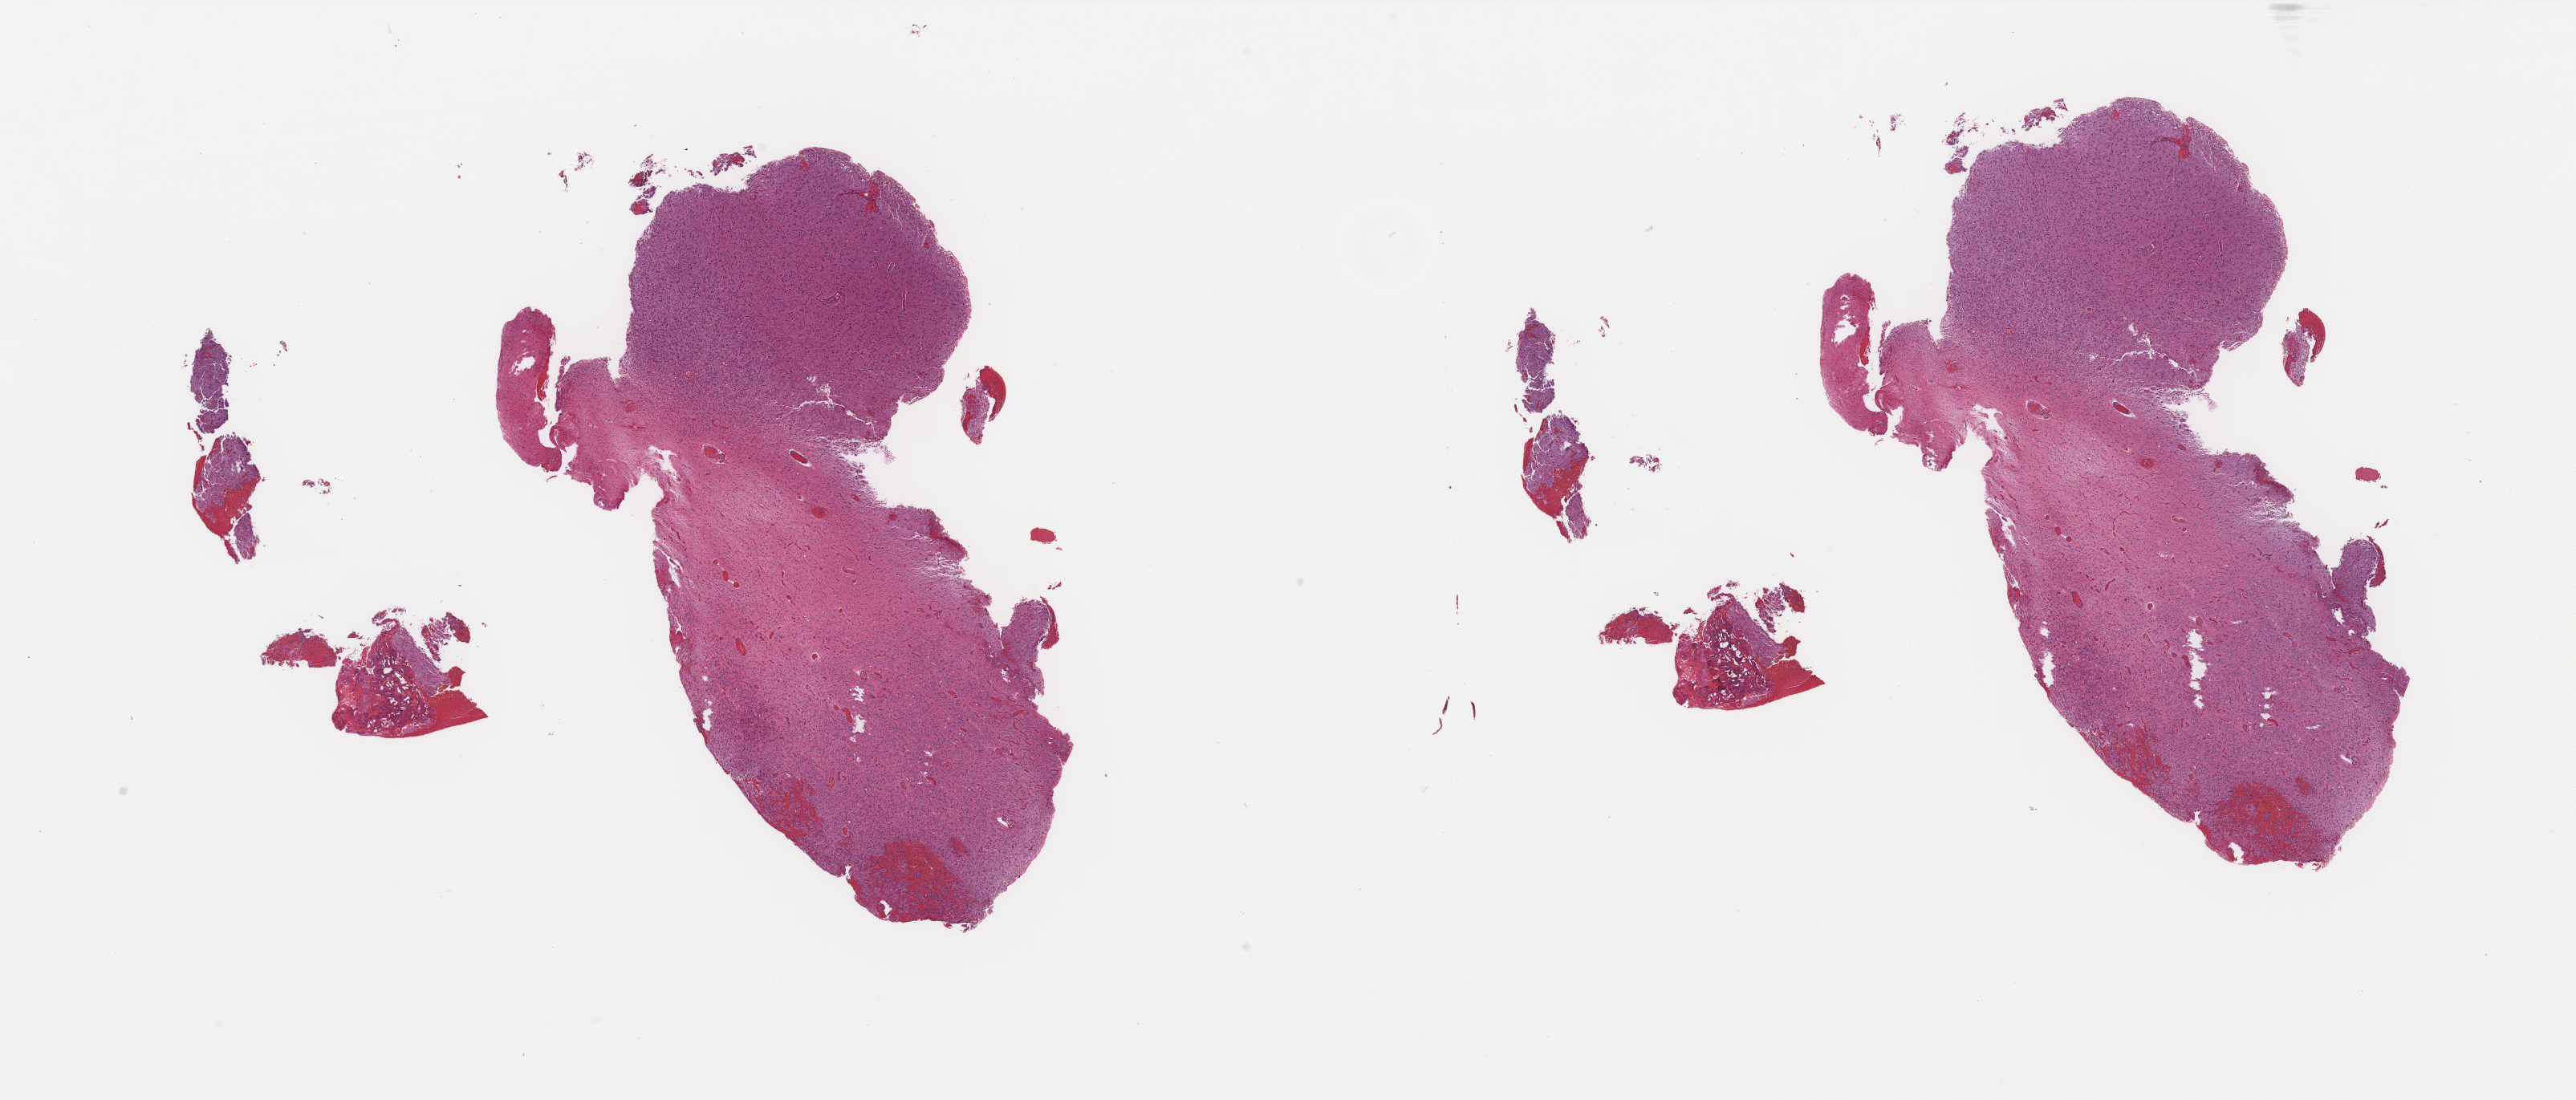
H&E-stained whole-slide image — shown as a low-resolution overview of the whole scanned area (about 25.7 x 11.0 mm). Formalin-fixed paraffin-embedded (FFPE) diagnostic section. Brain, primary tumour sample. Patient: male, age at initial diagnosis 62 years. Histologic grade: G3 (poorly differentiated).
Diagnosis: Mixed glioma (cerebrum).